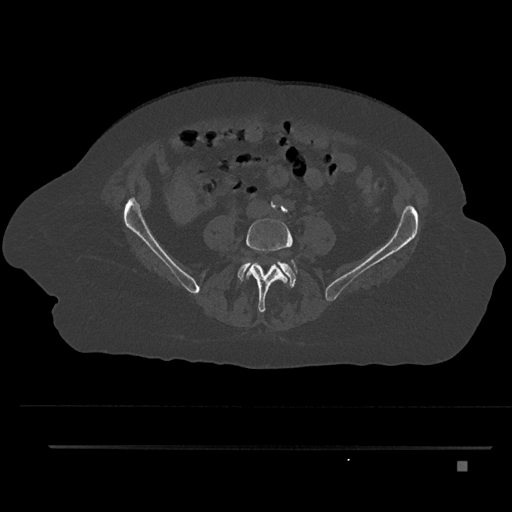
CT including the spine, one axial slice. Slice 70 of 797 in the series (ordered by position). Reconstruction kernel Br40s/3. Bone window (W 1800 / L 400 HU). 0.5 mm slice thickness. 512 × 512 image matrix, field of view 437 × 437 mm. Female patient, age 76 years. Case-level facts recorded for this patient, not image findings: primary cancer: lung; vertebrae with lytic lesions (as recorded): T11, L3.
Structures marked on this image (semi-automatic segmentation, software-assisted and operator-edited):
- L4 vertebra: bounding box <246,218,297,313> (left, top, right, bottom; pixels)
- L5 vertebra: <238,260,297,287>